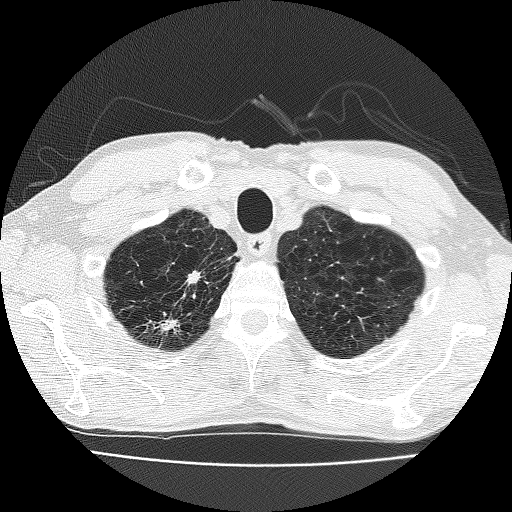
Axial slice from a low-dose chest CT screening exam. Third annual screen. Lung window (W 1500 / L -600 HU). 2 mm slice thickness. Lung (sharp) reconstruction kernel (FC51). 512 × 512 image matrix. Male, age 63 years at enrolment. Current smoker at enrolment.
Expert reader's lesion annotation, box from (x=143, y=256) to (x=223, y=340) px. Screening reader's record for this exam (one nodule recorded; not confirmed to be the boxed lesion): non-calcified nodule or mass ≥4 mm, right upper lobe, 17 × 10 mm, spiculated (stellate) margins, soft tissue attenuation, pre-existing on the prior screen: yes; interval growth: yes. Participant outcome: lung cancer diagnosed 28 days after this screen — adenocarcinoma, NOS, right upper lobe, moderately differentiated (G2), stage IIIB (AJCC 6th edition), 17 mm at pathology.